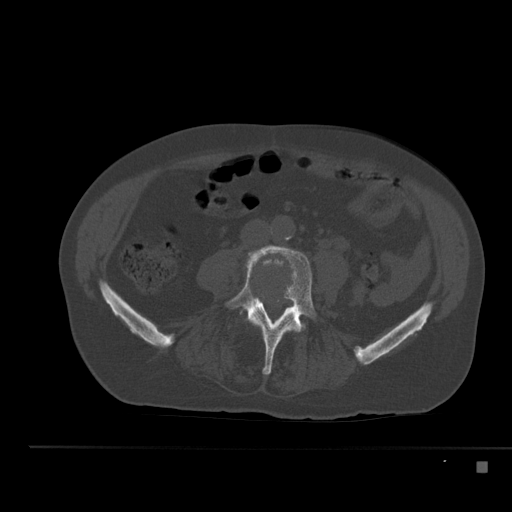
CT including the spine, one axial slice. Position 142 of 517 along the scan axis. Bone window (W 1800 / L 400 HU). 1.5 mm slice thickness. 512 × 512 image matrix, field of view 408 × 408 mm. Male patient, age 70 years. Case-level facts recorded for this patient, not image findings: primary cancer: renal.
Outlined on this slice (semi-automatically segmented with operator editing):
- L4 vertebra: bounding box <226,245,317,375> (left, top, right, bottom; pixels)